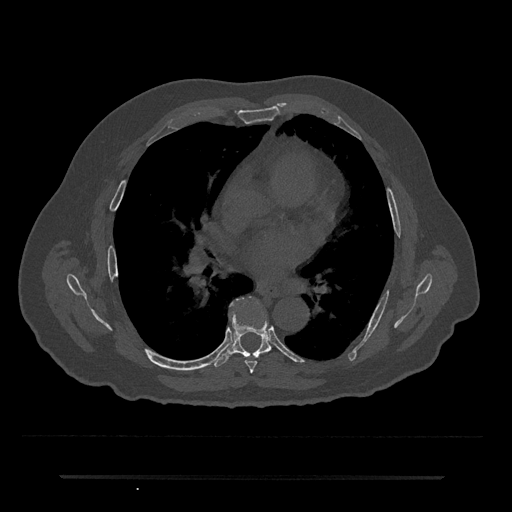
CT including the spine, one axial slice; position 408 of 797 along the scan axis; reconstruction kernel Br40s/3; bone window (W 1800 / L 400 HU); 0.5 mm slice thickness; 512 × 512 image matrix. Male patient, age 69 years. From the clinical record (not read from this slice): primary cancer: prostate.
Annotated regions visible in this slice (semi-automatic segmentation, software-assisted and operator-edited):
- T6 vertebra: bounding box [x1, y1, x2, y2] px = [245, 360, 257, 373]
- T7 vertebra: [214, 304, 272, 367]